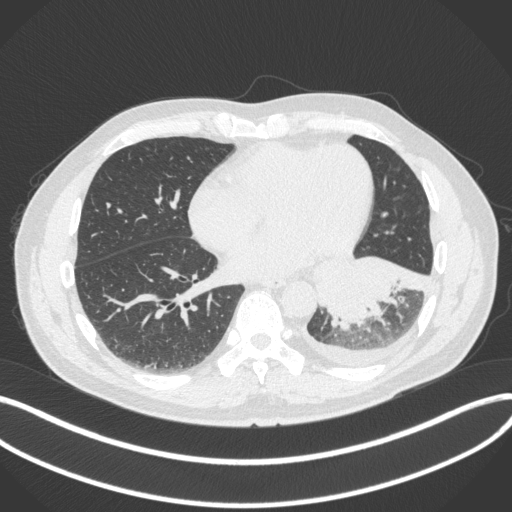
Chest CT, one axial slice. Position 136 of 350 along the scan axis. Reconstruction kernel B31f. 120 kVp. Lung window (W 1500 / L -600 HU). 1 mm slice thickness. 512 × 512 image matrix. Male patient, age 58 years. Case-level facts recorded for this patient, not image findings: clinical TNM (as recorded): T3 N1 M1b; histopathological grade: G3.
Outlined on this slice (rectangle marked by the reading radiologist):
- lung tumour (recorded histology: small cell carcinoma): bounding box <316,250,430,331> (left, top, right, bottom; pixels)